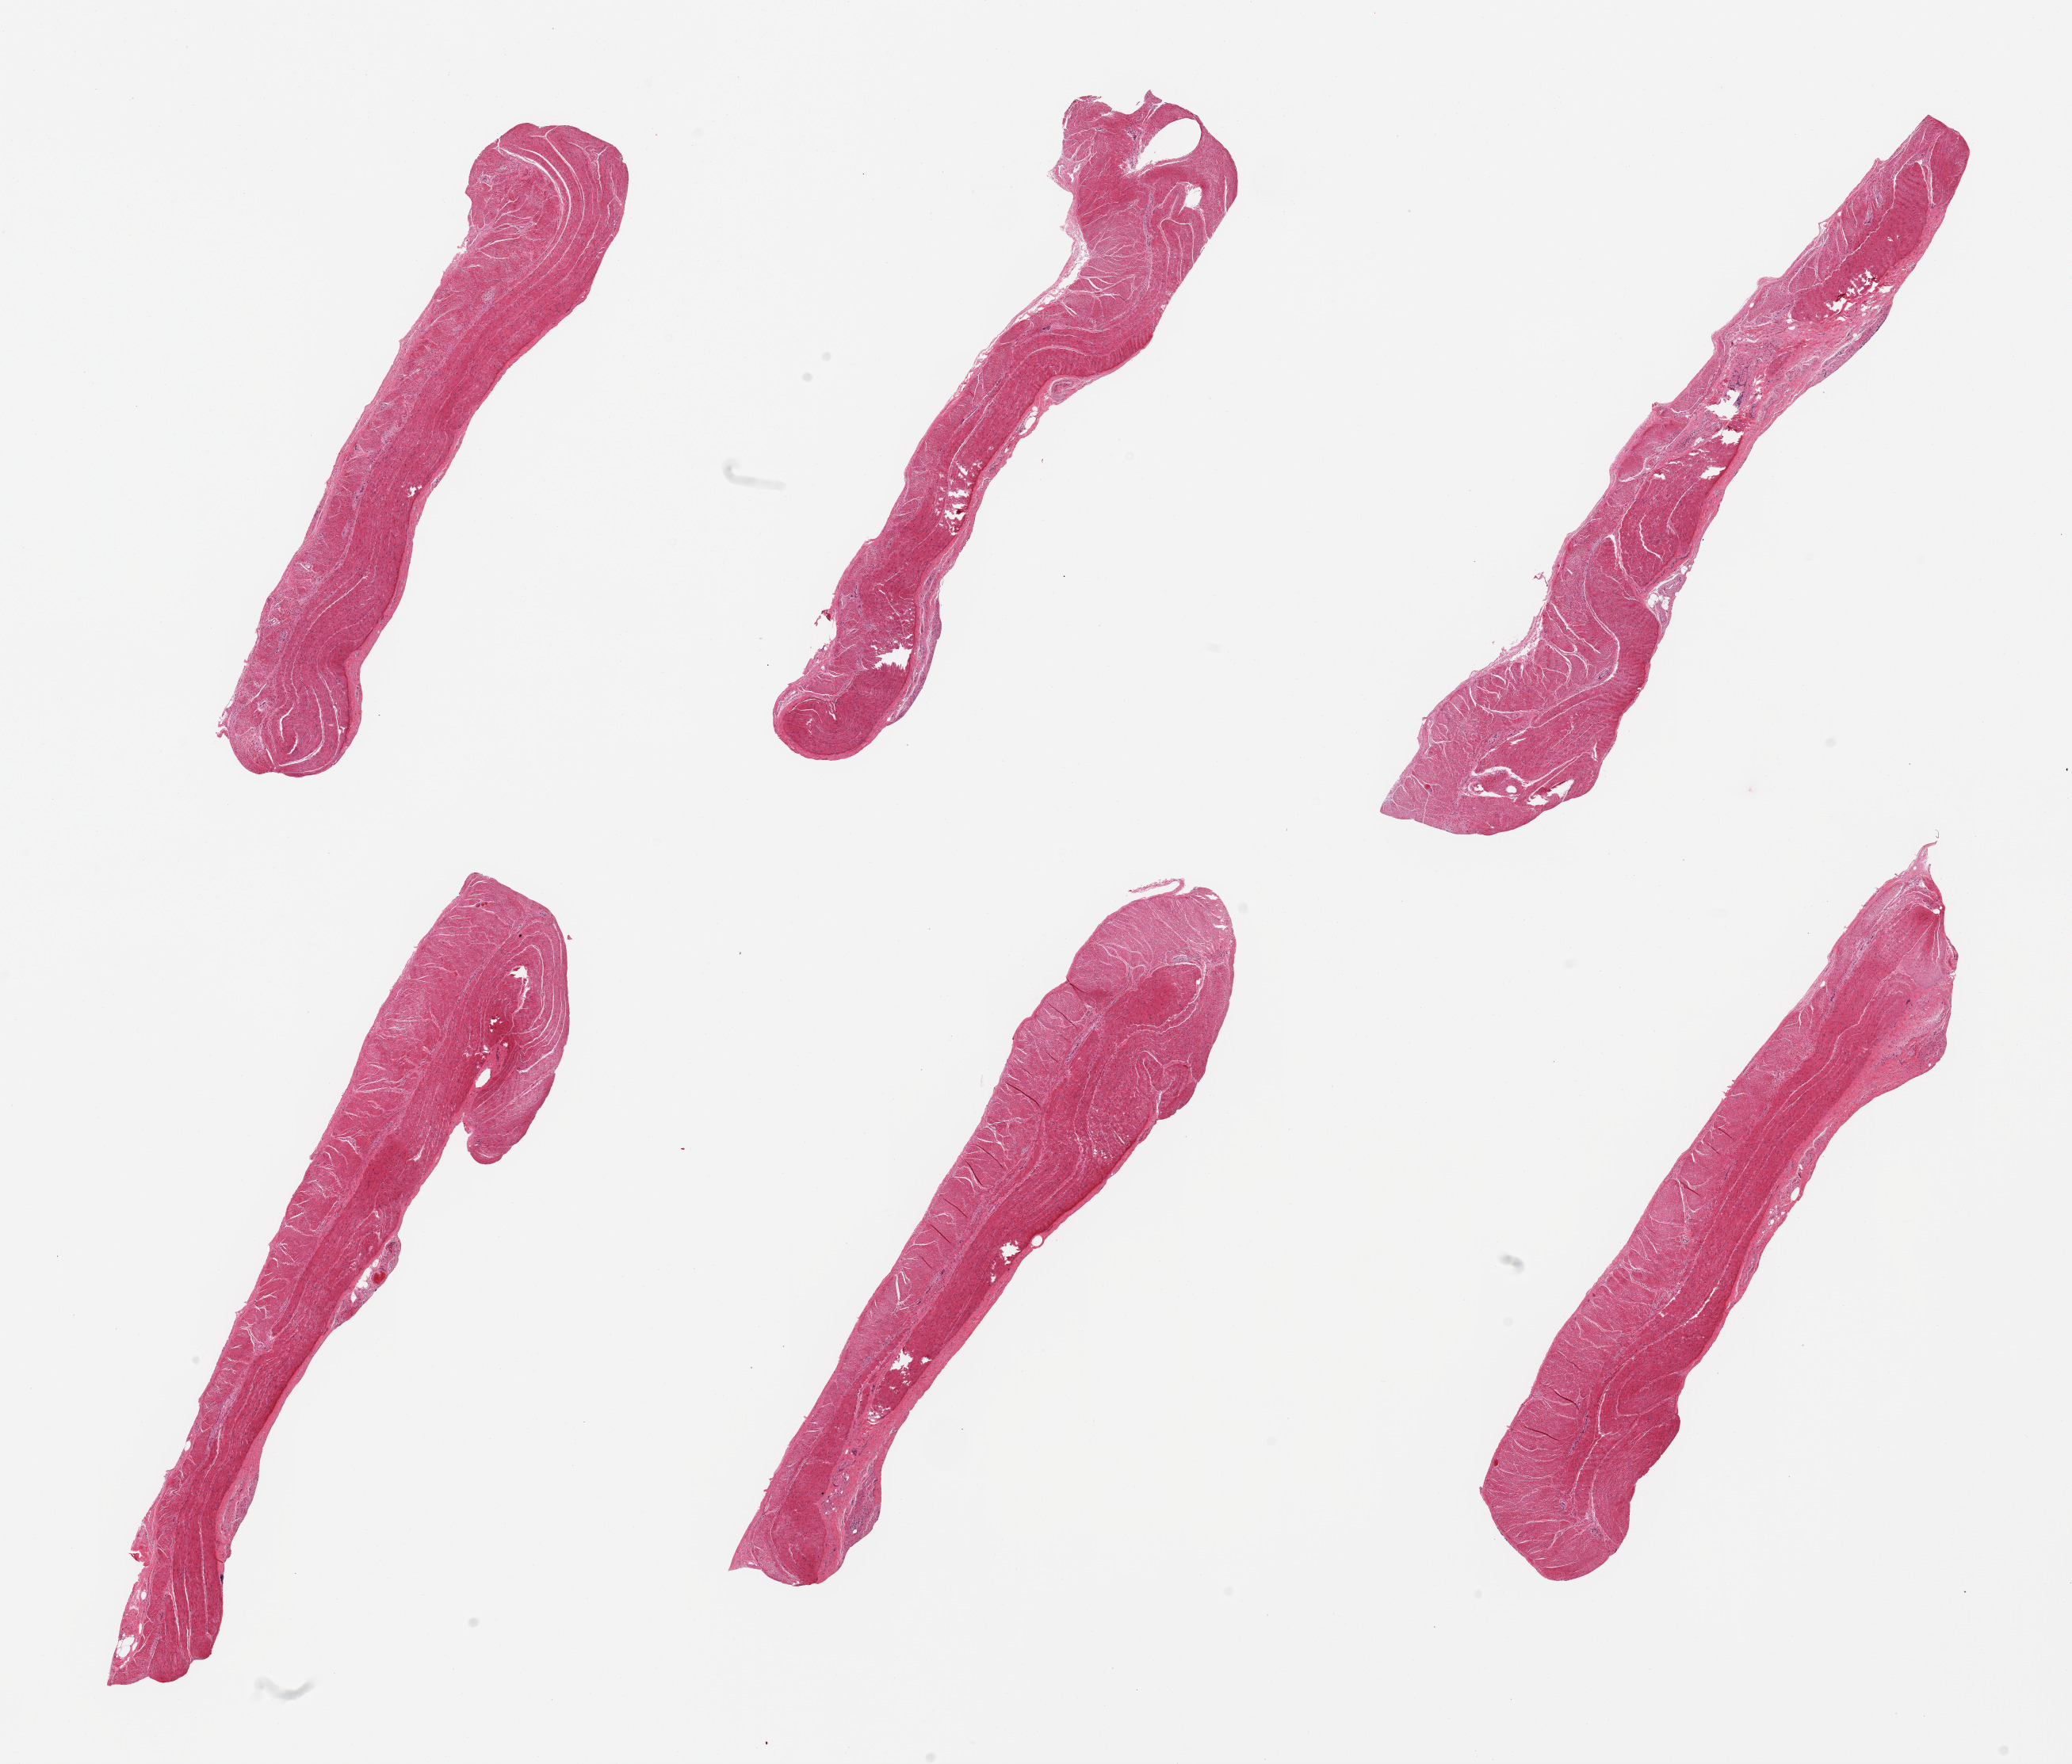
Whole-slide image, hematoxylin and eosin (H&E) stain, brightfield, low-resolution overview of the scanned area, about 20.7 x 17.6 mm (acquisition: 20x scan), PAXgene-fixed, paraffin-embedded tissue, sampled site (target tissue): sigmoid colon, tissue donor sample. Donor: male.
- reviewer comment on this tissue sample: 6 pieces; target muscularis, well trimmed